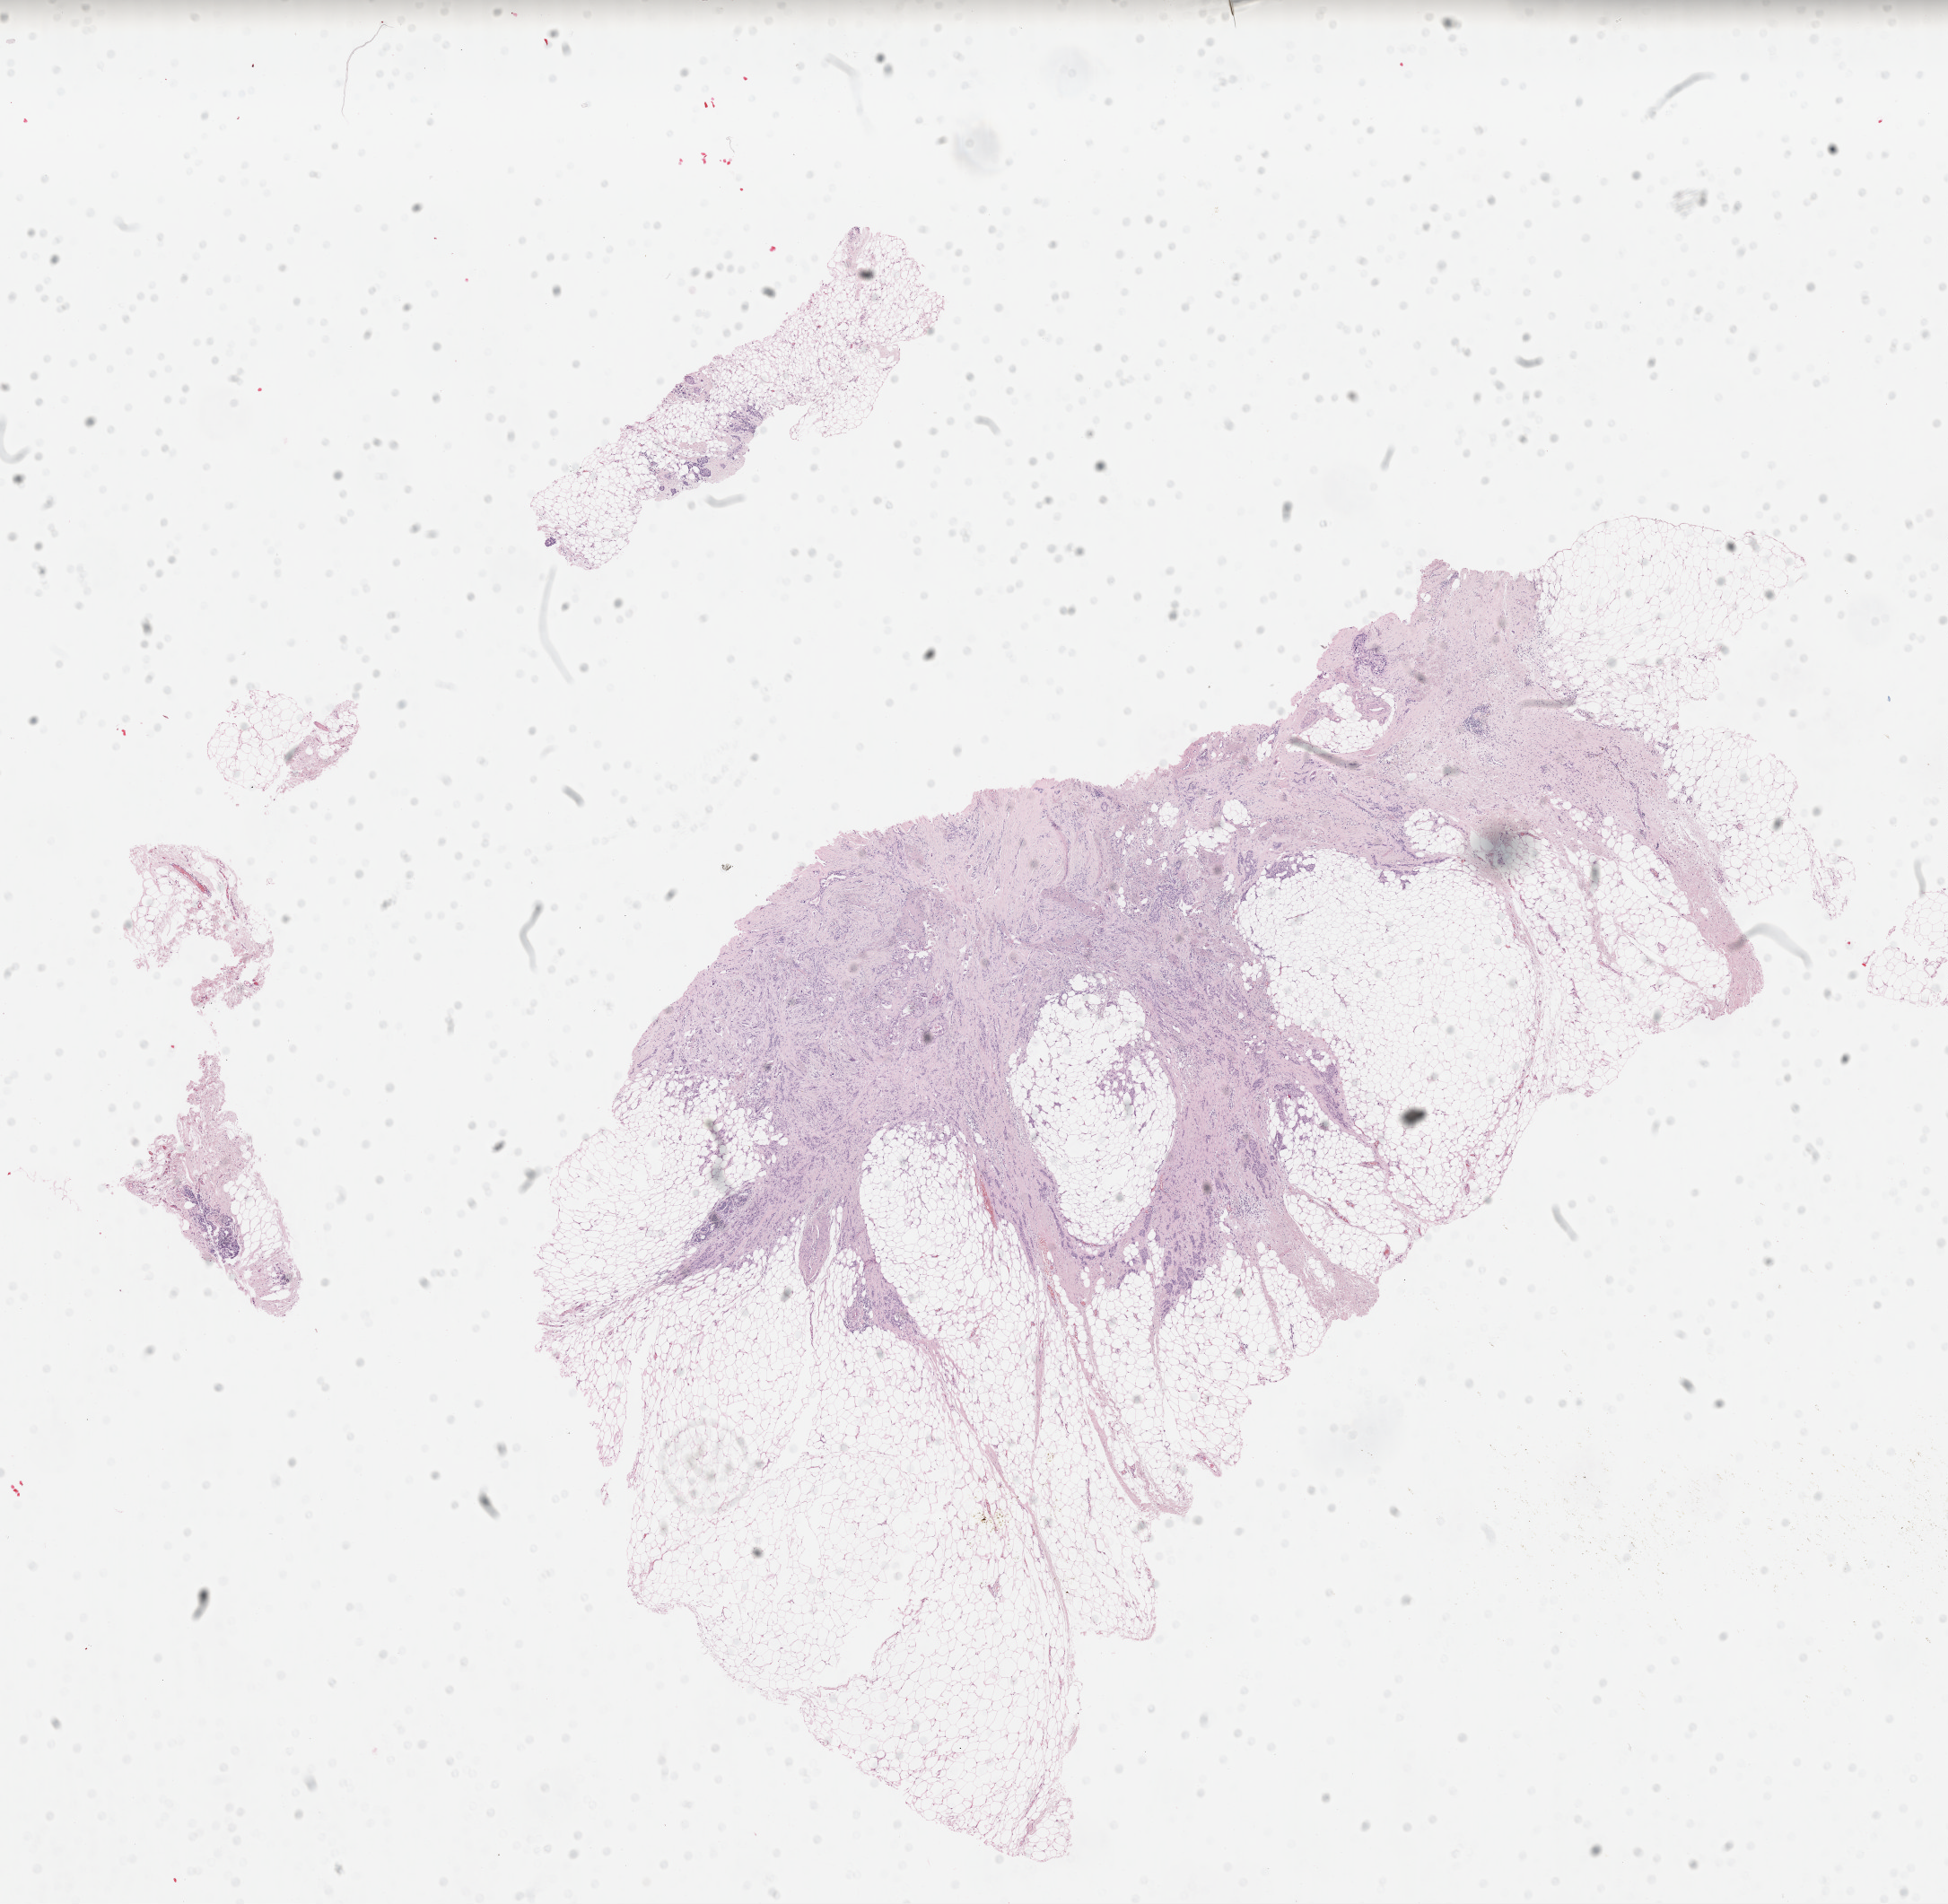
H&E-stained whole-slide image — low-resolution overview of the scanned area, about 17.2 x 16.8 mm (from a 40x scan); FFPE section; primary tumour sample from the breast. Patient: female, age at initial diagnosis 64 years.
Lymph nodes positive (case pathology): 0 of 1 examined. AJCC pathologic stage: IA (7th edition). TNM: T1c N0 M0. Pathologic diagnosis: Infiltrating duct carcinoma, NOS.